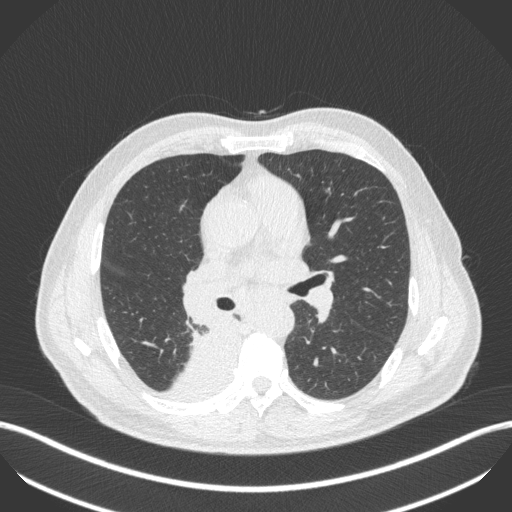
Chest CT, one axial slice. Position 263 of 451 along the scan axis. Reconstruction kernel B31f. 100 kVp. Lung window (W 1500 / L -600 HU). 512 × 512 image matrix, field of view 400 × 400 mm. Male patient, age 61 years. From the clinical record (not read from this slice): clinical TNM (as recorded): T1 N0 M0.
Outlined on this slice (rectangle marked by the reading radiologist):
- lung tumour (recorded histology: small cell carcinoma): bounding box <156,324,245,398> (left, top, right, bottom; pixels)